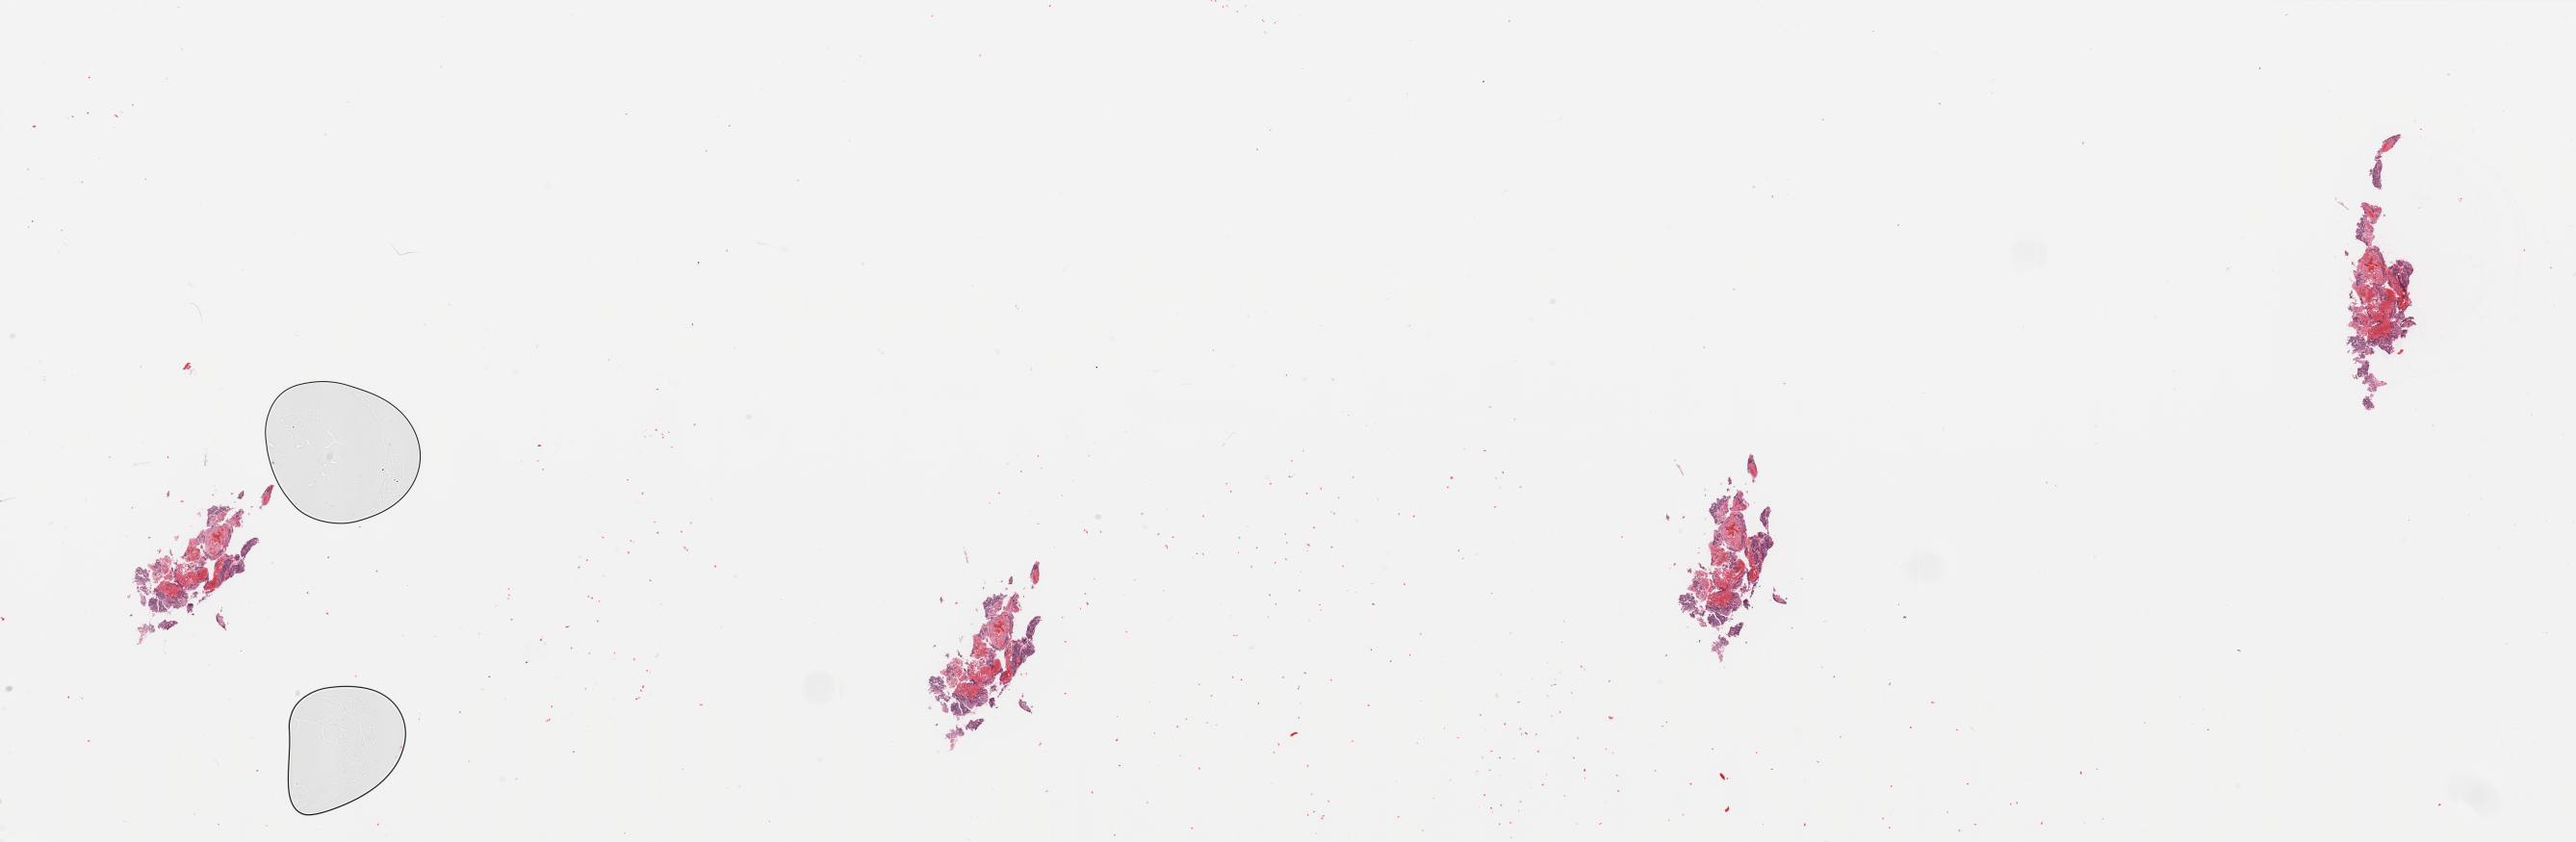
Digitized H&E-stained tissue section (whole slide) — whole scanned area (about 42.3 x 13.8 mm) shown as a low-resolution overview. Uterus, tumour tissue. 56-year-old female patient.
Histologic diagnosis: Endometrioid adenocarcinoma, NOS.